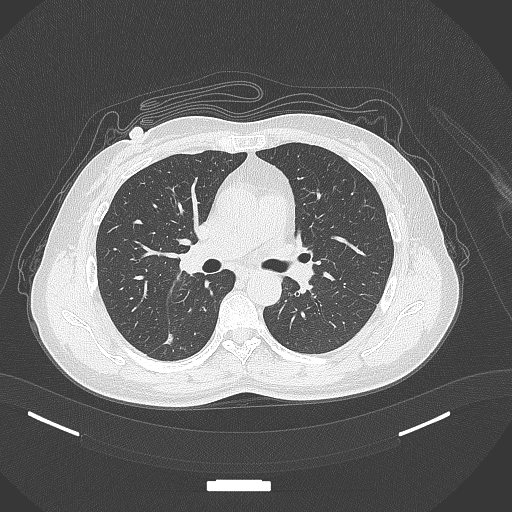
Chest CT, one axial slice. Position 180 of 352 along the scan axis. Lung window (W 1500 / L -600 HU). 1 mm slice thickness. 512 × 512 image matrix. Patient: female, 55 years. Case-level facts recorded for this patient, not image findings: clinical TNM (as recorded): T1c N1 M0.
Annotated regions visible in this slice (rectangle marked by the reading radiologist):
- lung tumour (recorded histology: adenocarcinoma): bounding box <160,328,183,348> (left, top, right, bottom; pixels)